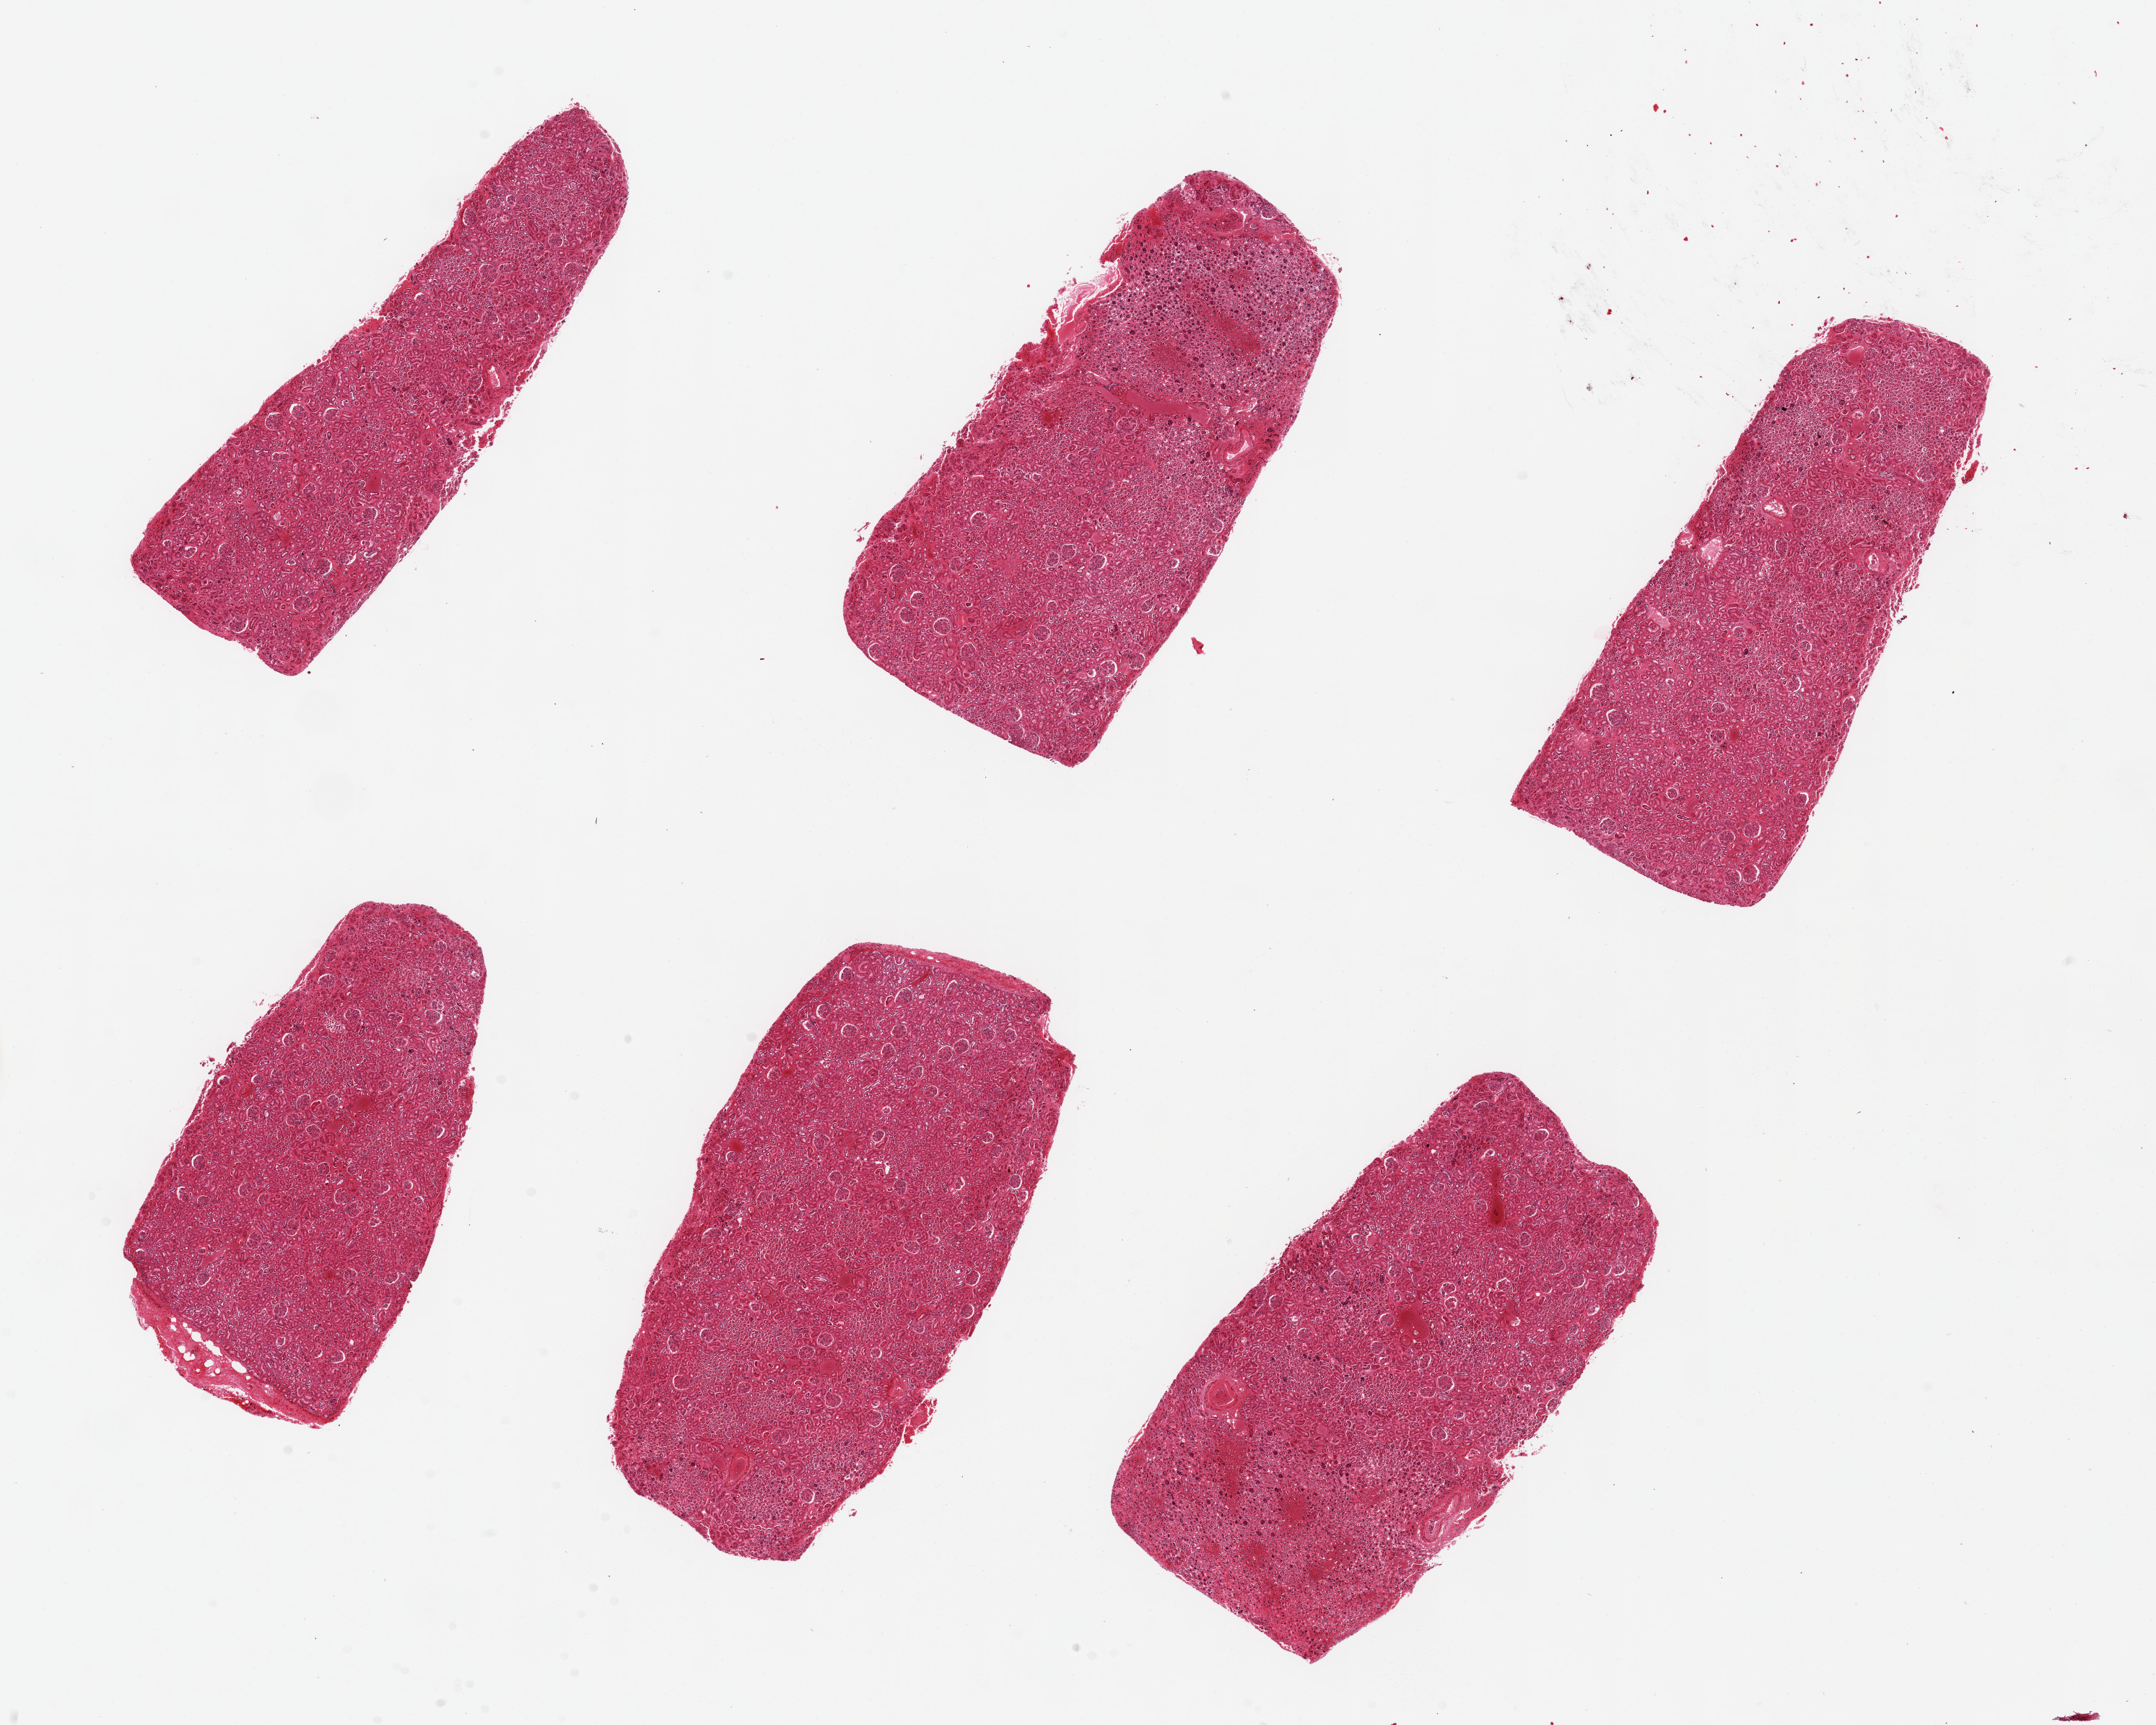
Digitized hematoxylin and eosin (H&E)-stained section — whole scanned area (about 23.6 x 18.9 mm) shown as a low-resolution overview. PAXgene-fixed, paraffin-embedded tissue. Sampled site (target tissue): renal cortex. Donor tissue sample. Female donor.
Reviewer comment on this tissue sample: 6 pieces ~7x3mm.